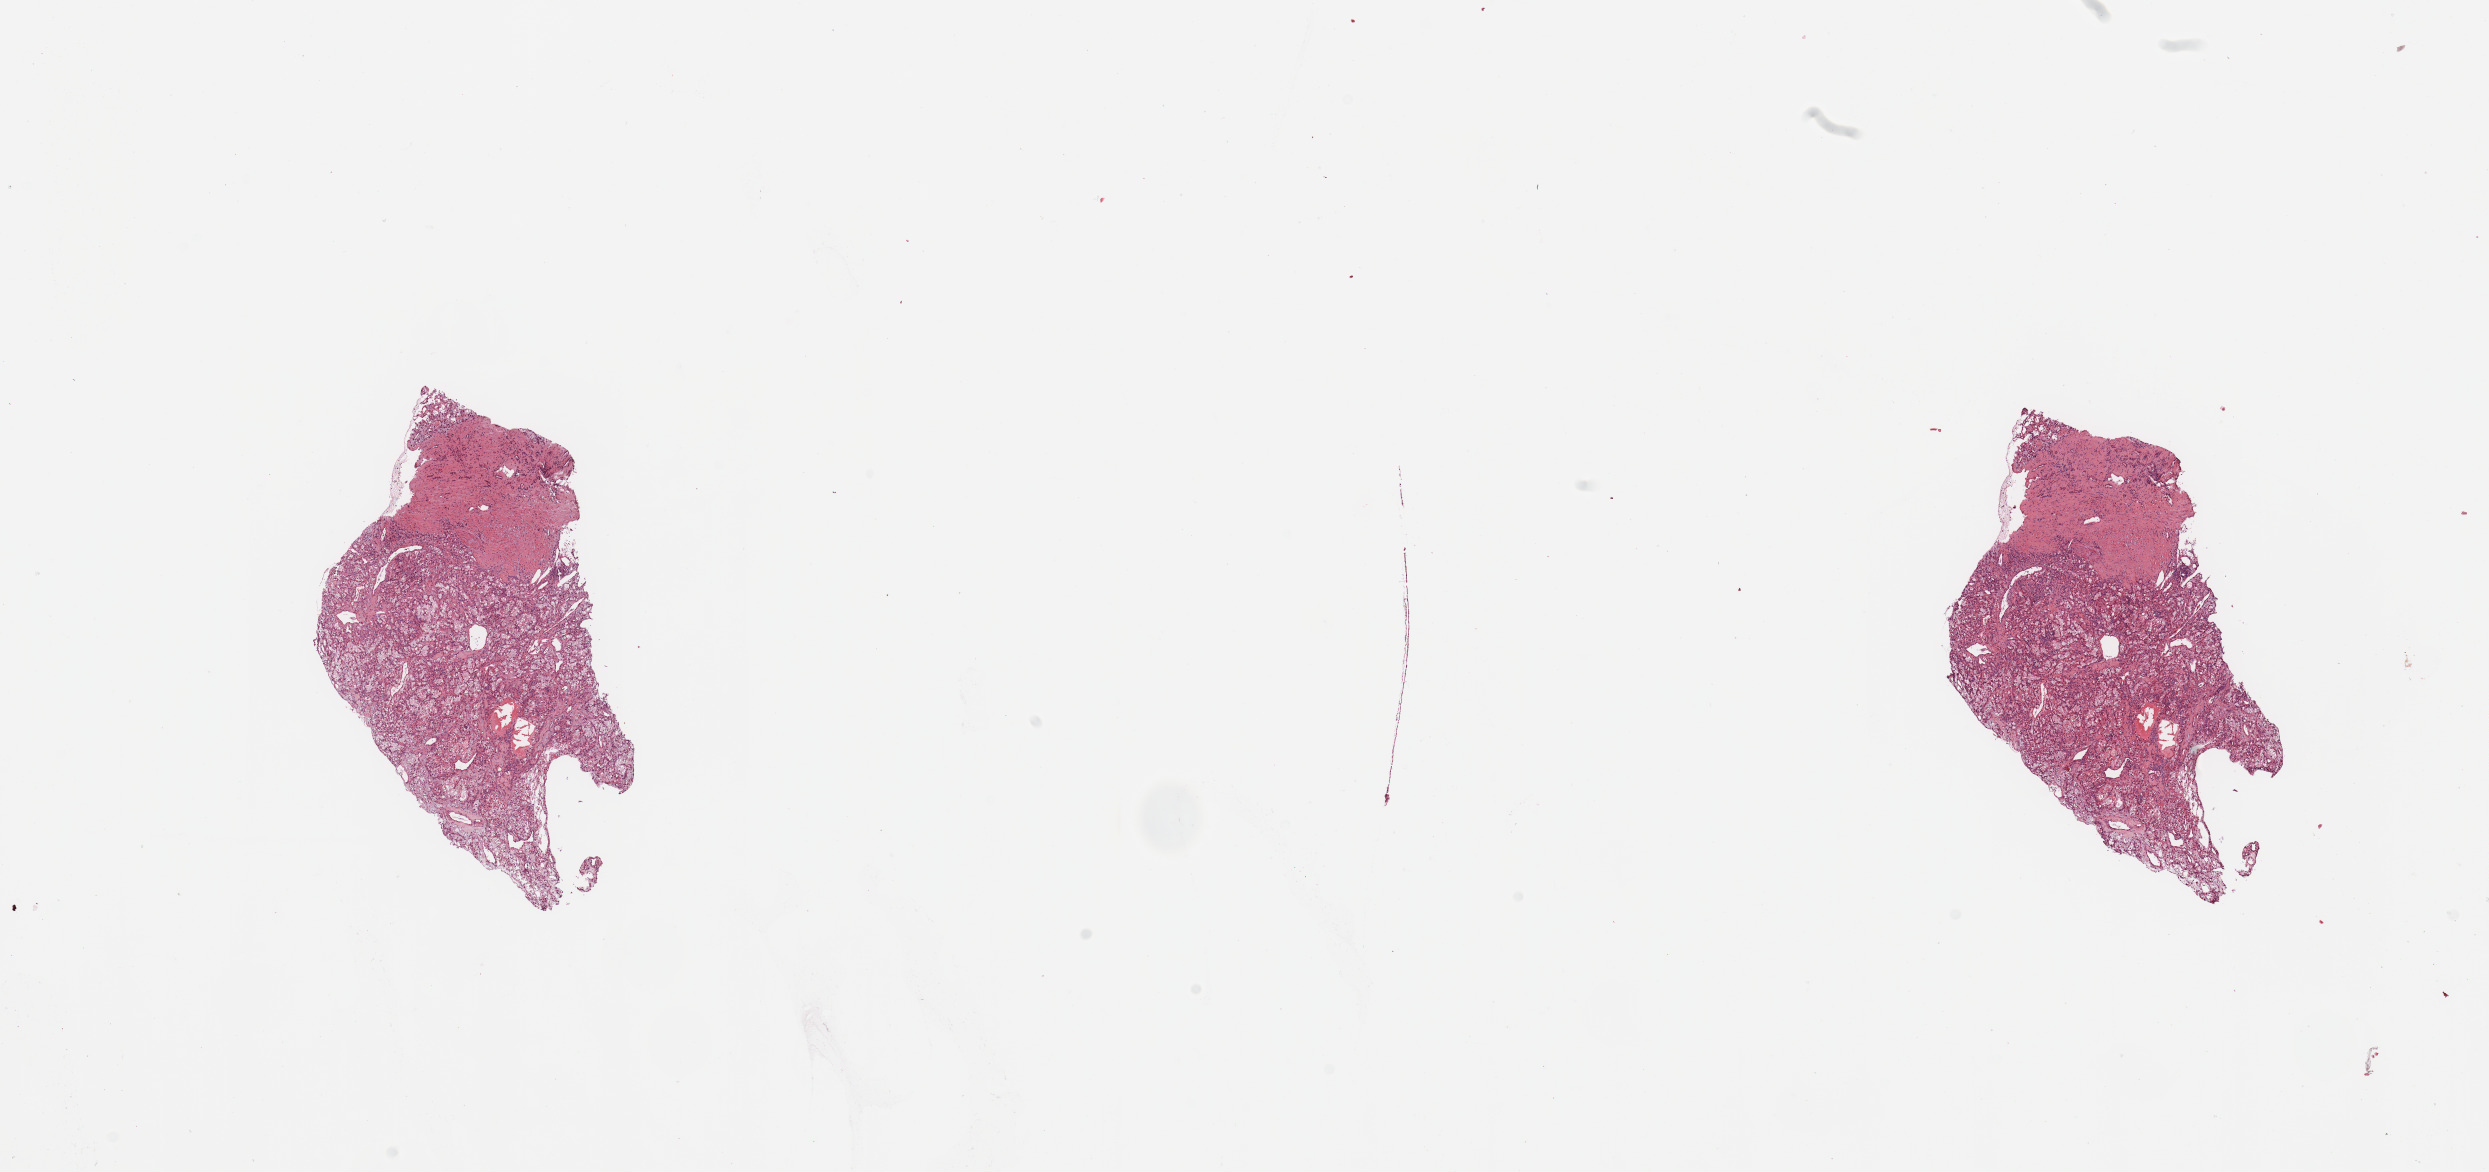
Hematoxylin and eosin (H&E) stained whole-slide image, a low-resolution overview of the entire scanned area, about 19.7 x 9.3 mm. Kidney, tumour tissue. Patient: male, age 59 years. Histologic grade: G2 (moderately differentiated).
AJCC pathologic stage: III. Primary tumour site (as recorded): lower pole. Diagnosis: Renal cell carcinoma, NOS.